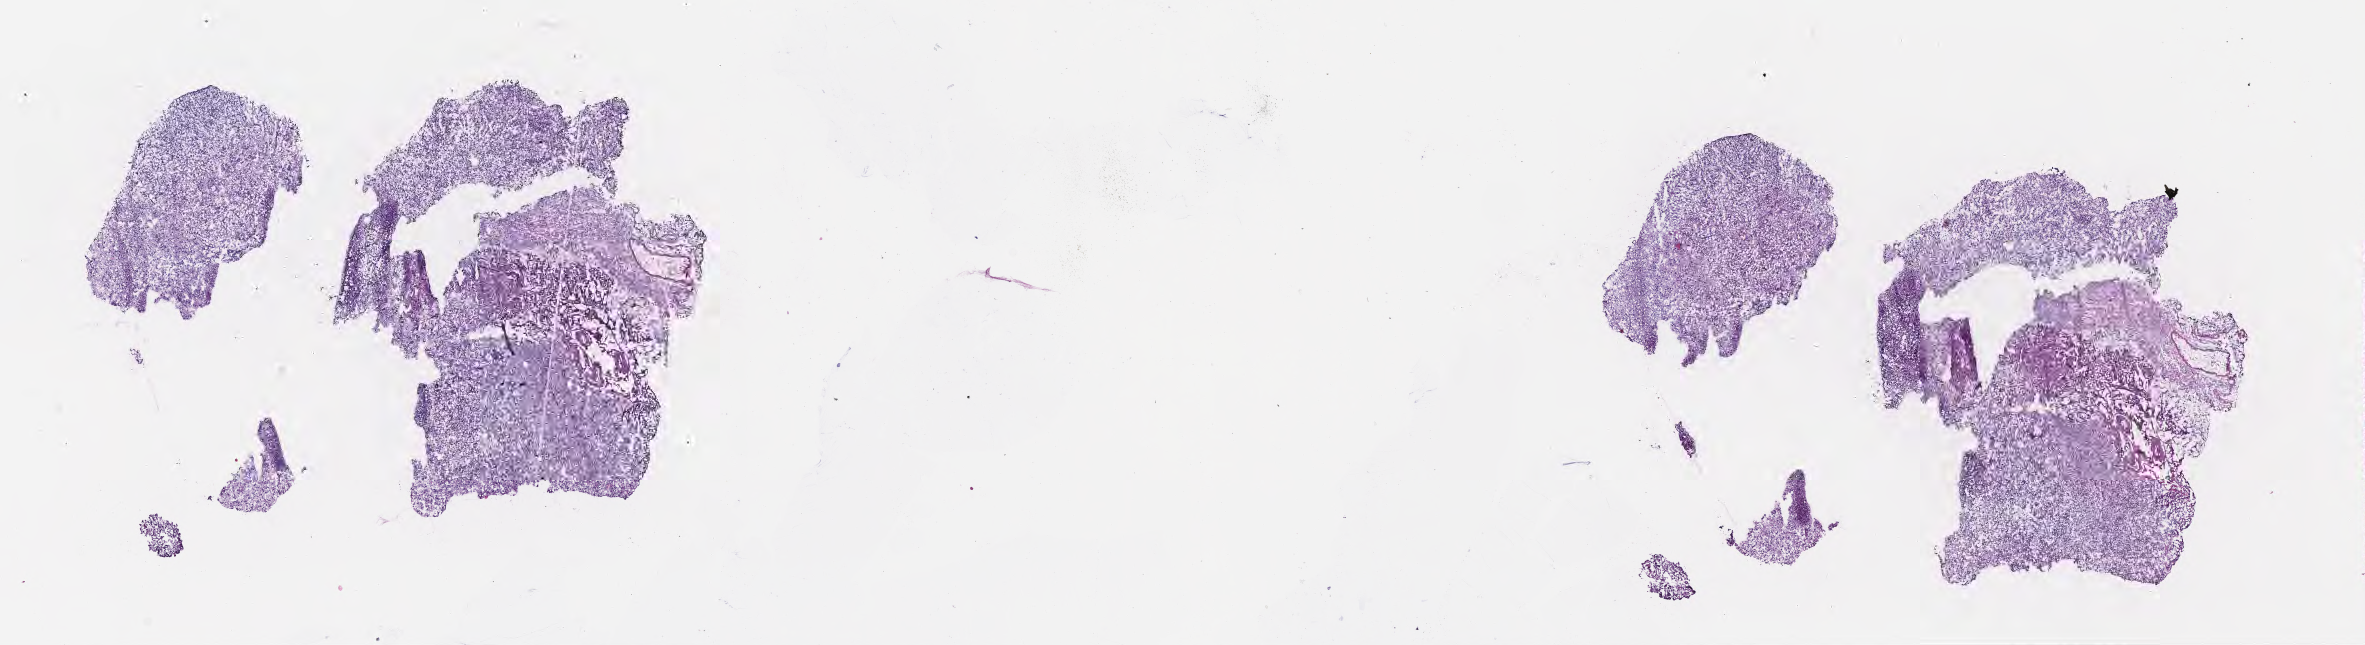
Digitized H&E-stained section, a low-resolution overview of the entire scanned area, about 19.1 x 5.2 mm. Cryosection. Specimen: primary tumor. Site: brain. Male patient; age at initial diagnosis 66 years. Pathologist review of this section (percent, as recorded): tumor cells 88%, tumor nuclei 93%, stromal cells 3%, necrosis 2%, normal cells 7%. Infiltration values recorded for this section: lymphocyte infiltration 0%, monocyte infiltration 0%, neutrophil infiltration 0%.
Histologic diagnosis: Gliosarcoma. Section: top of the tissue portion.